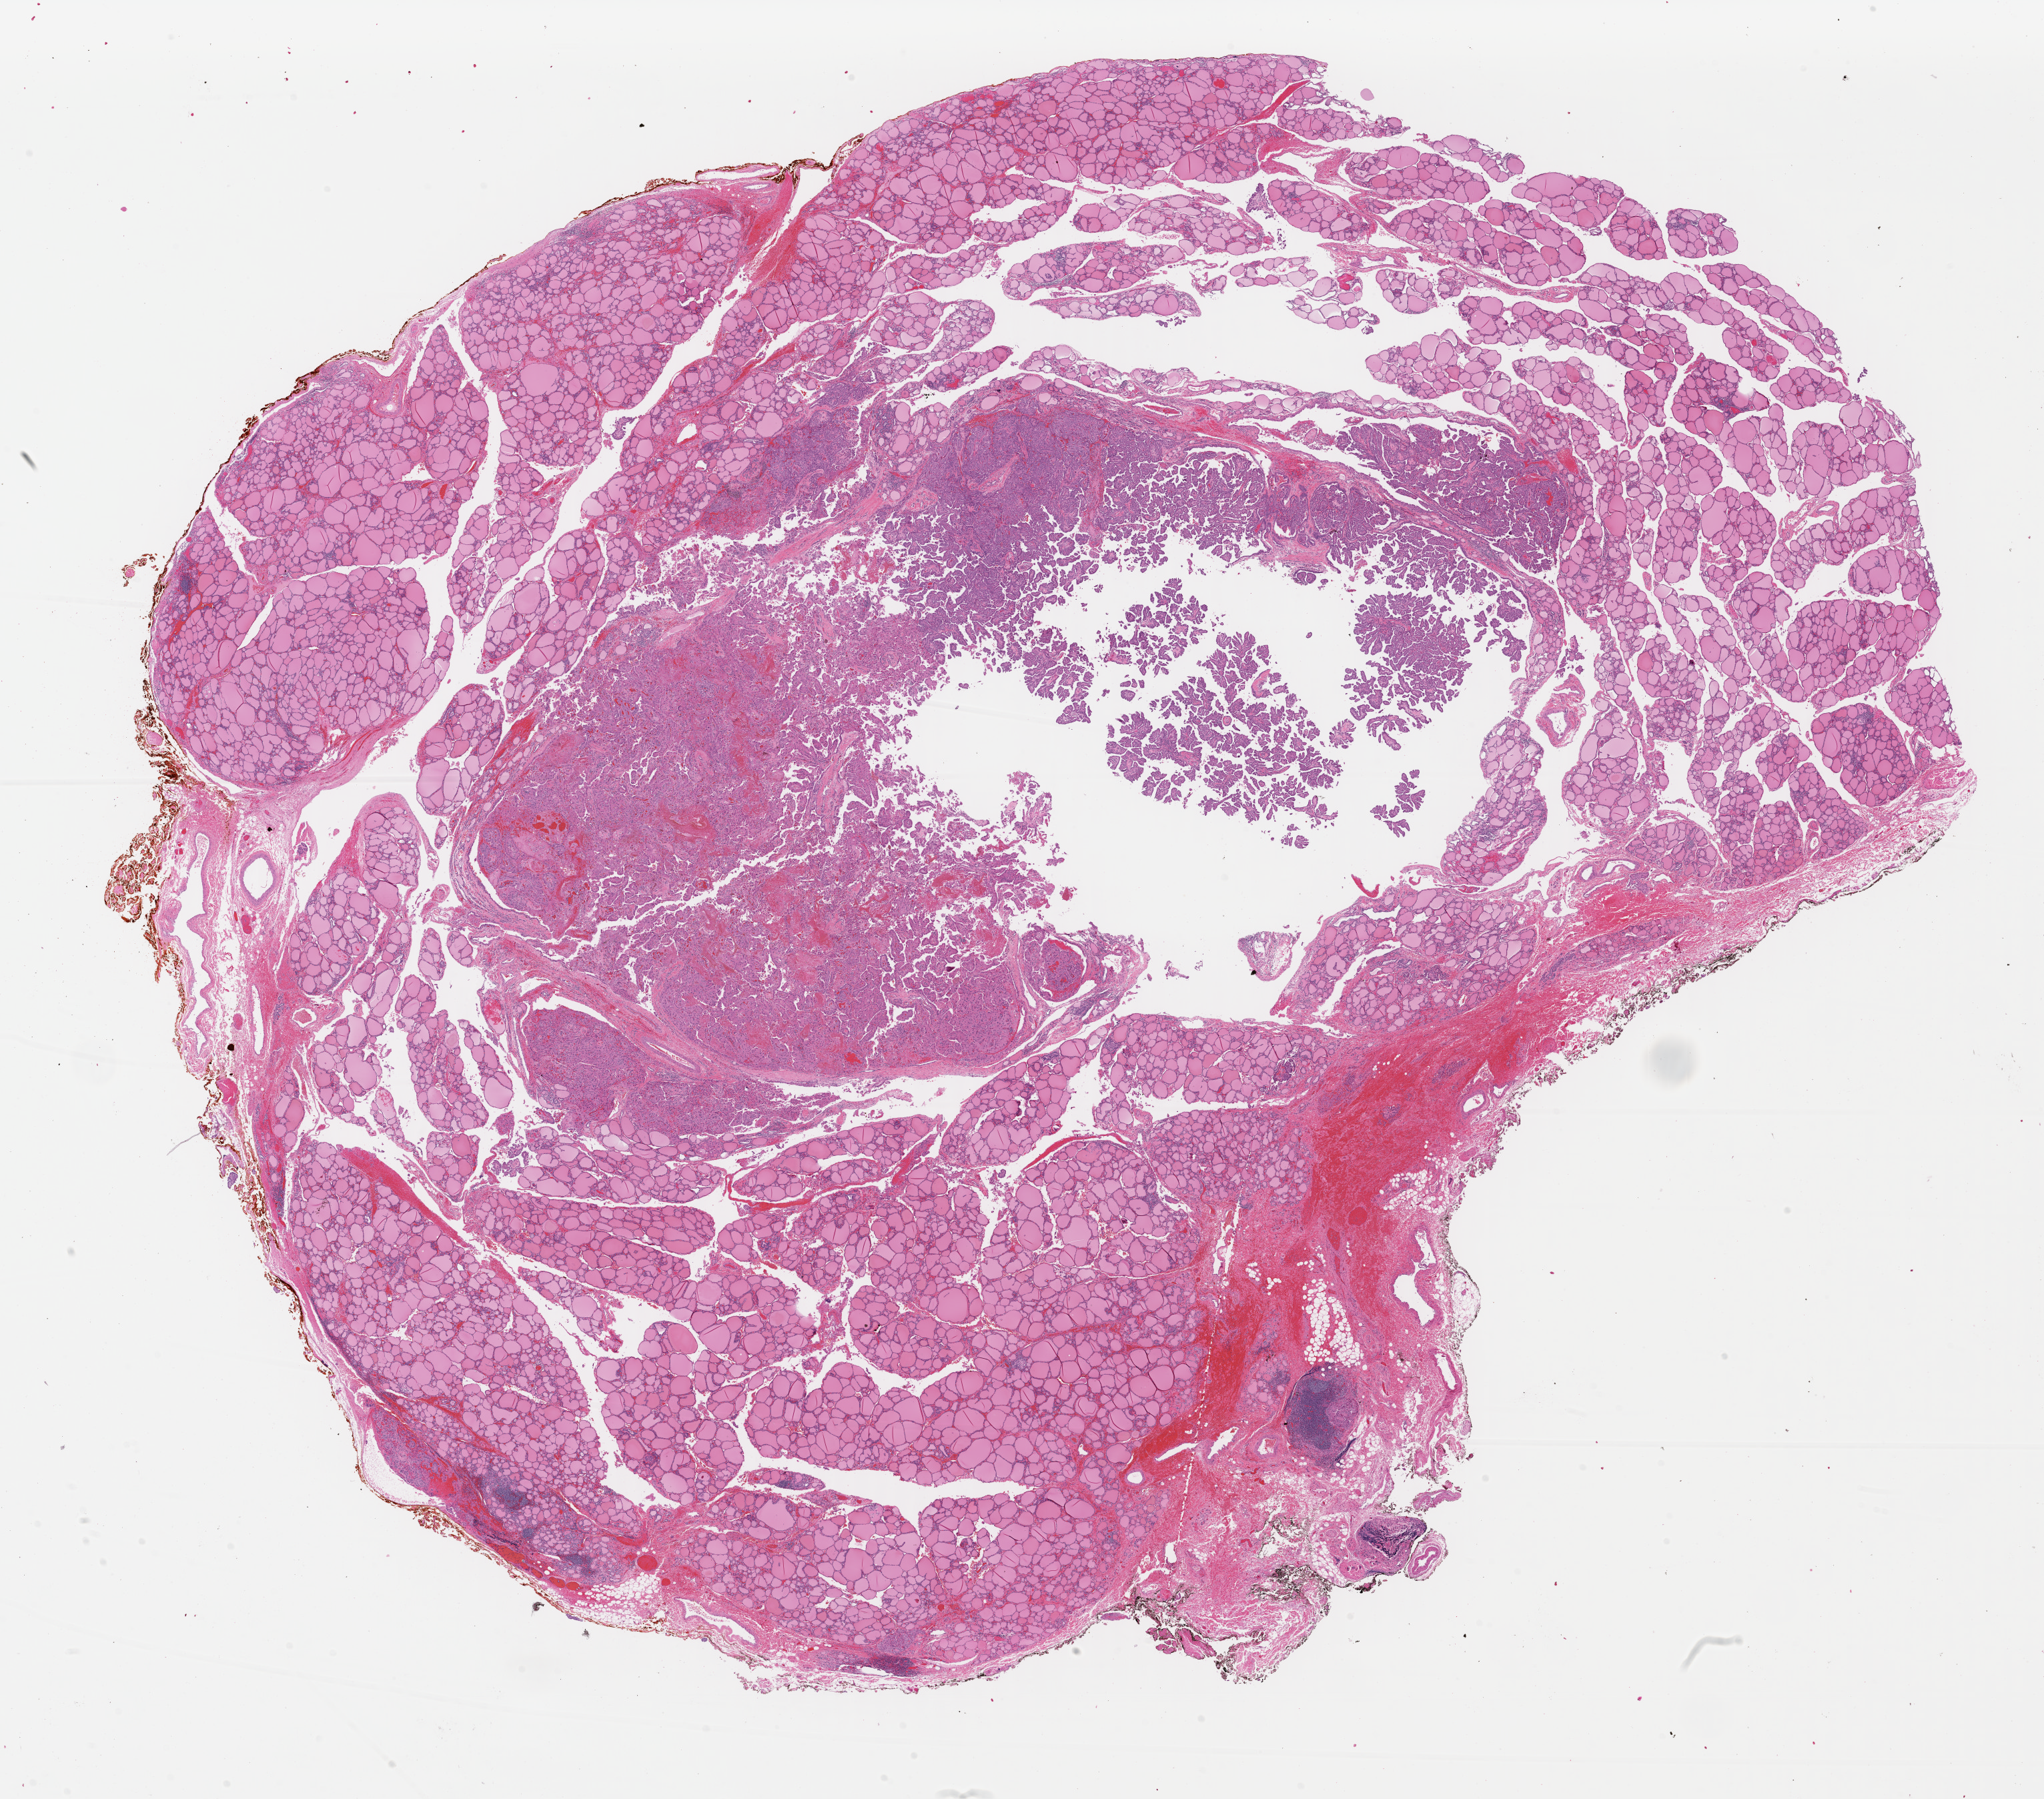
Digitized Hematoxylin and eosin (H&E) stained tissue section (whole slide), a low-resolution overview of the entire scanned area, about 24.1 x 21.2 mm, FFPE section, primary tumour sample from the thyroid. Male, age 27 years at initial diagnosis.
AJCC pathologic stage: I (6th edition). Histologic diagnosis: Papillary adenocarcinoma, NOS (thyroid gland).